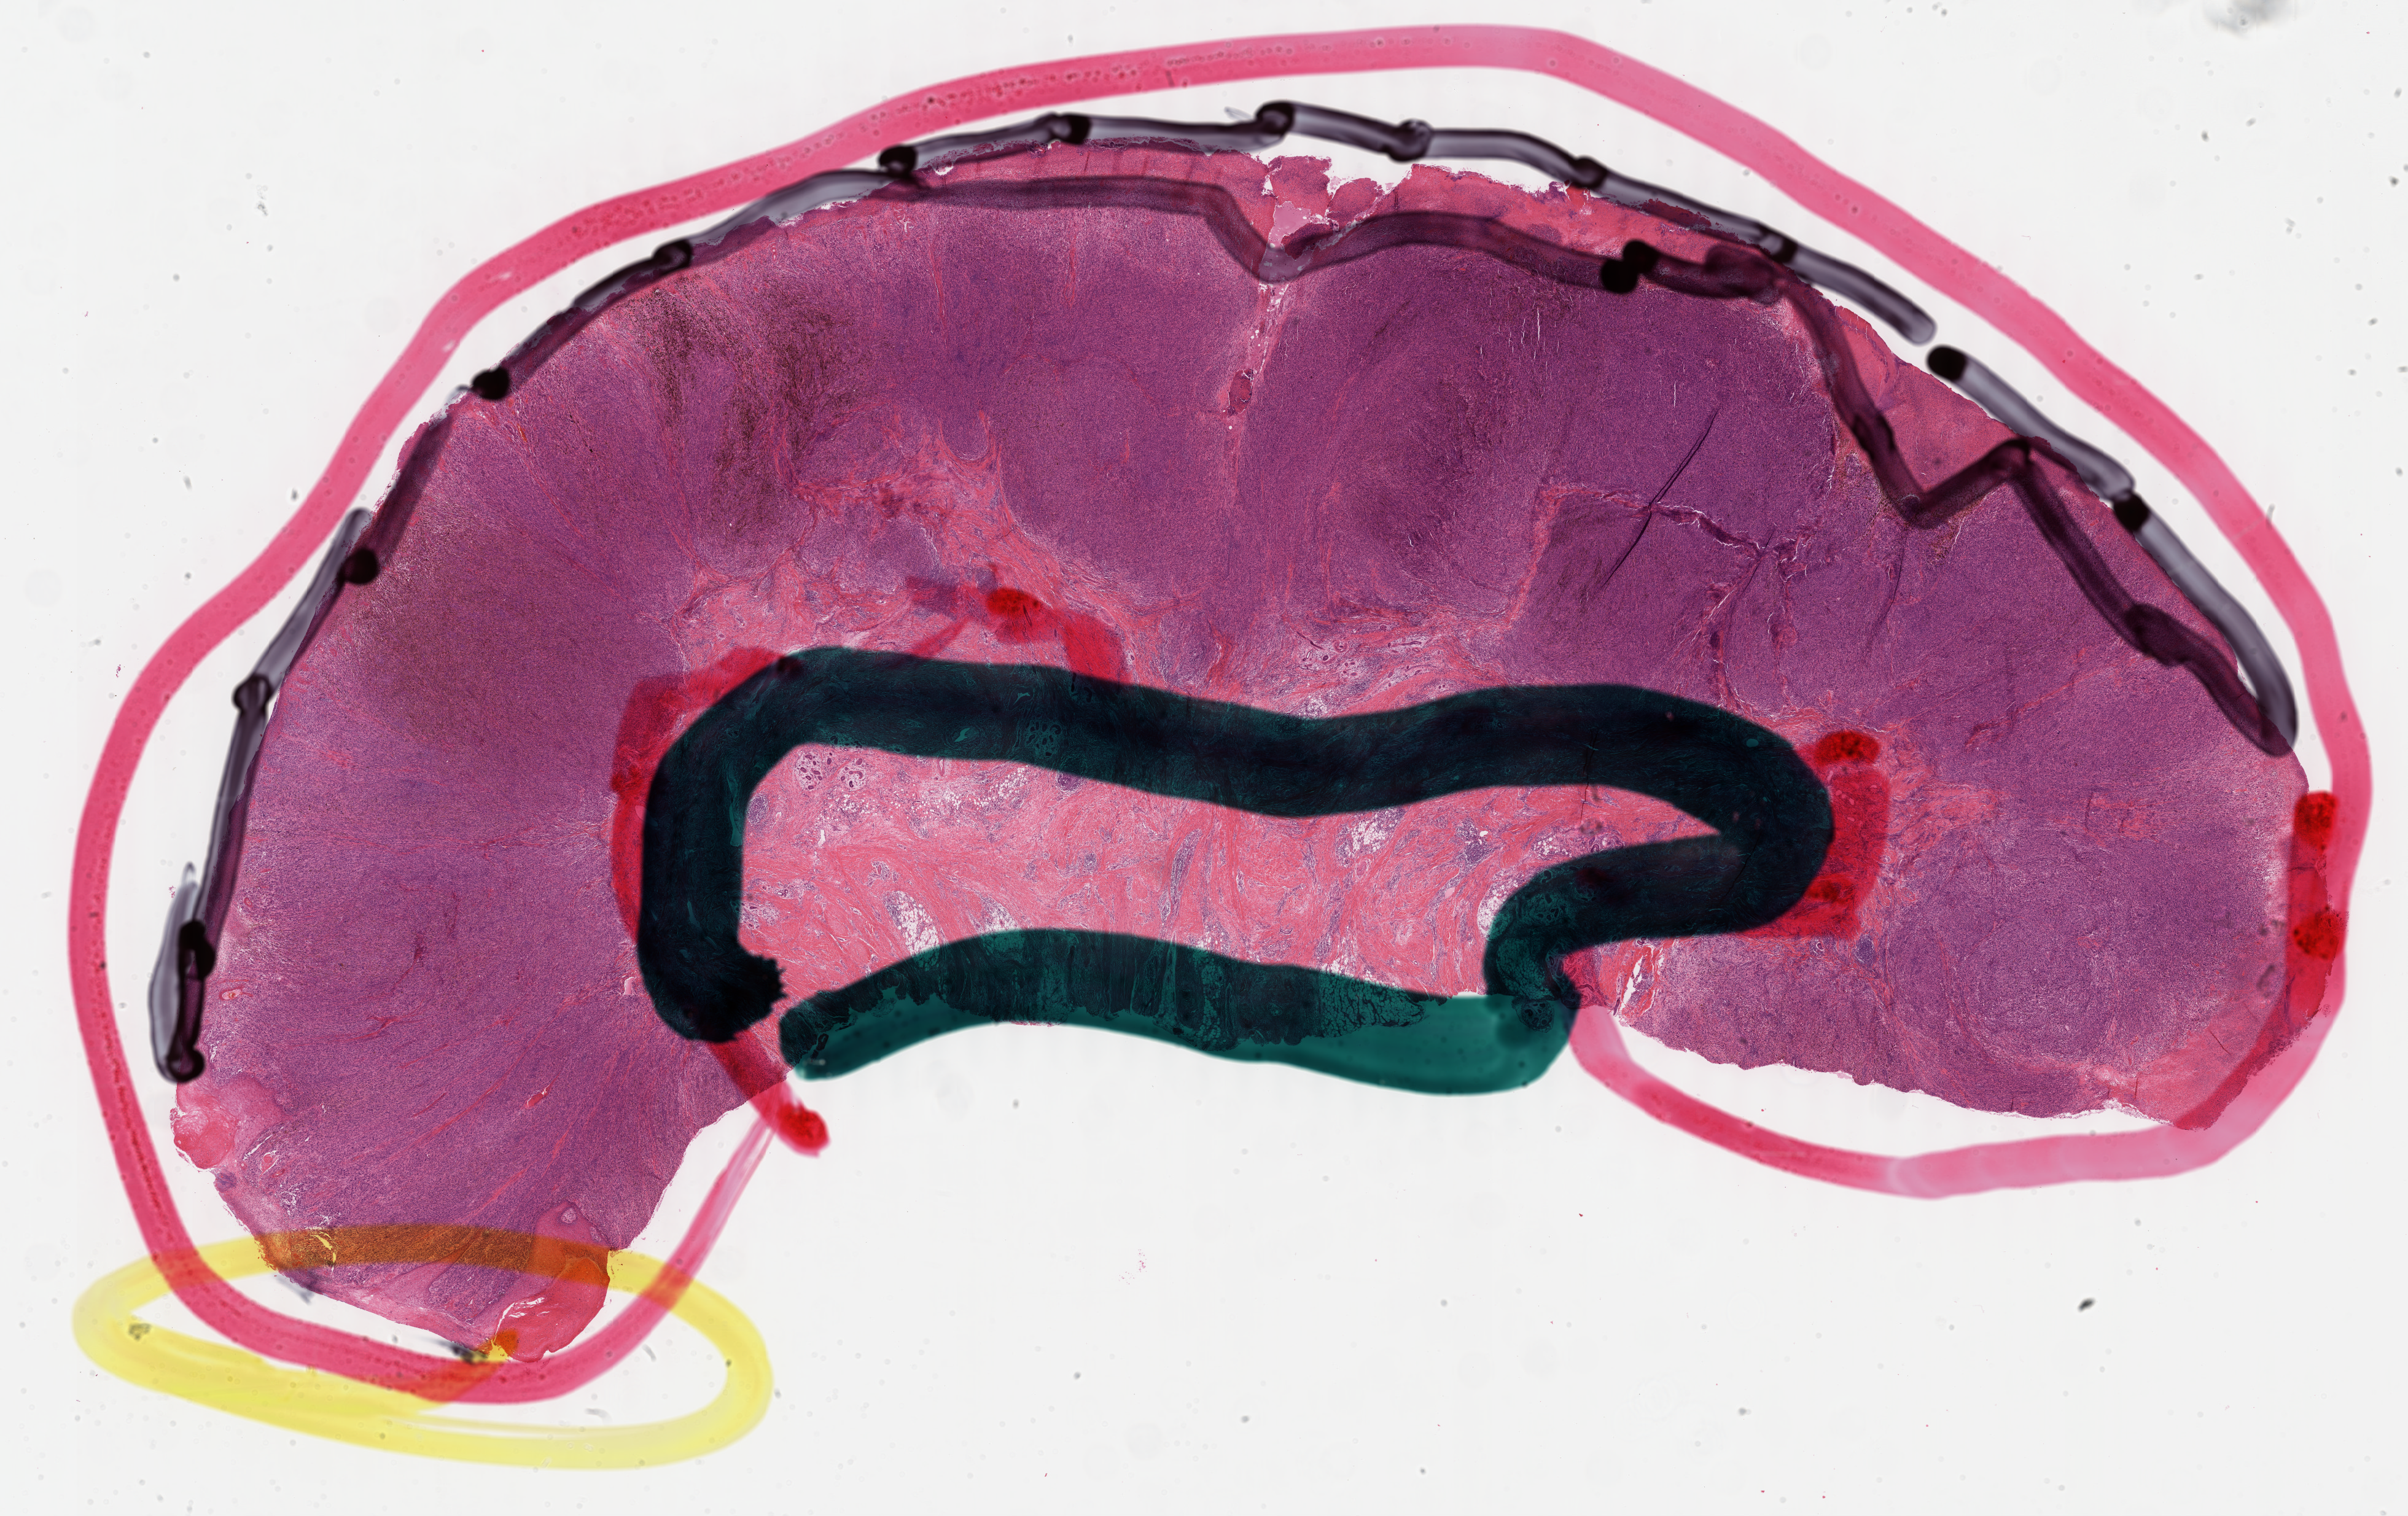
Digitized H&E tissue section (whole slide) — whole scanned area (about 31.7 x 20.0 mm) shown as a low-resolution overview. Formalin-fixed paraffin-embedded (FFPE) diagnostic section. Sample: primary tumour, skin. Female patient; age at initial diagnosis 58 years.
• histologic diagnosis: Malignant melanoma, NOS